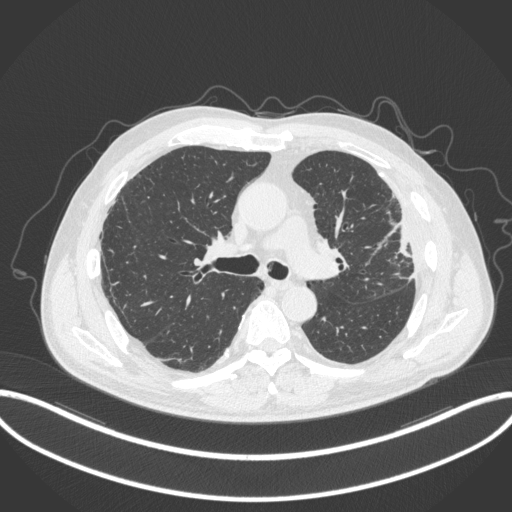
Chest CT, one axial slice. Position 216 of 382 along the scan axis. Reconstruction kernel B31f. Lung window (W 1500 / L -600 HU). 512 × 512 image matrix, field of view 415 × 415 mm. Male patient, age 64 years. Case-level facts recorded for this patient, not image findings: clinical TNM (as recorded): T4 N1 M0.
Outlined on this slice (bounding box drawn by a radiologist):
- lung tumour (recorded histology: adenocarcinoma): box from (x=386, y=215) to (x=418, y=263) px